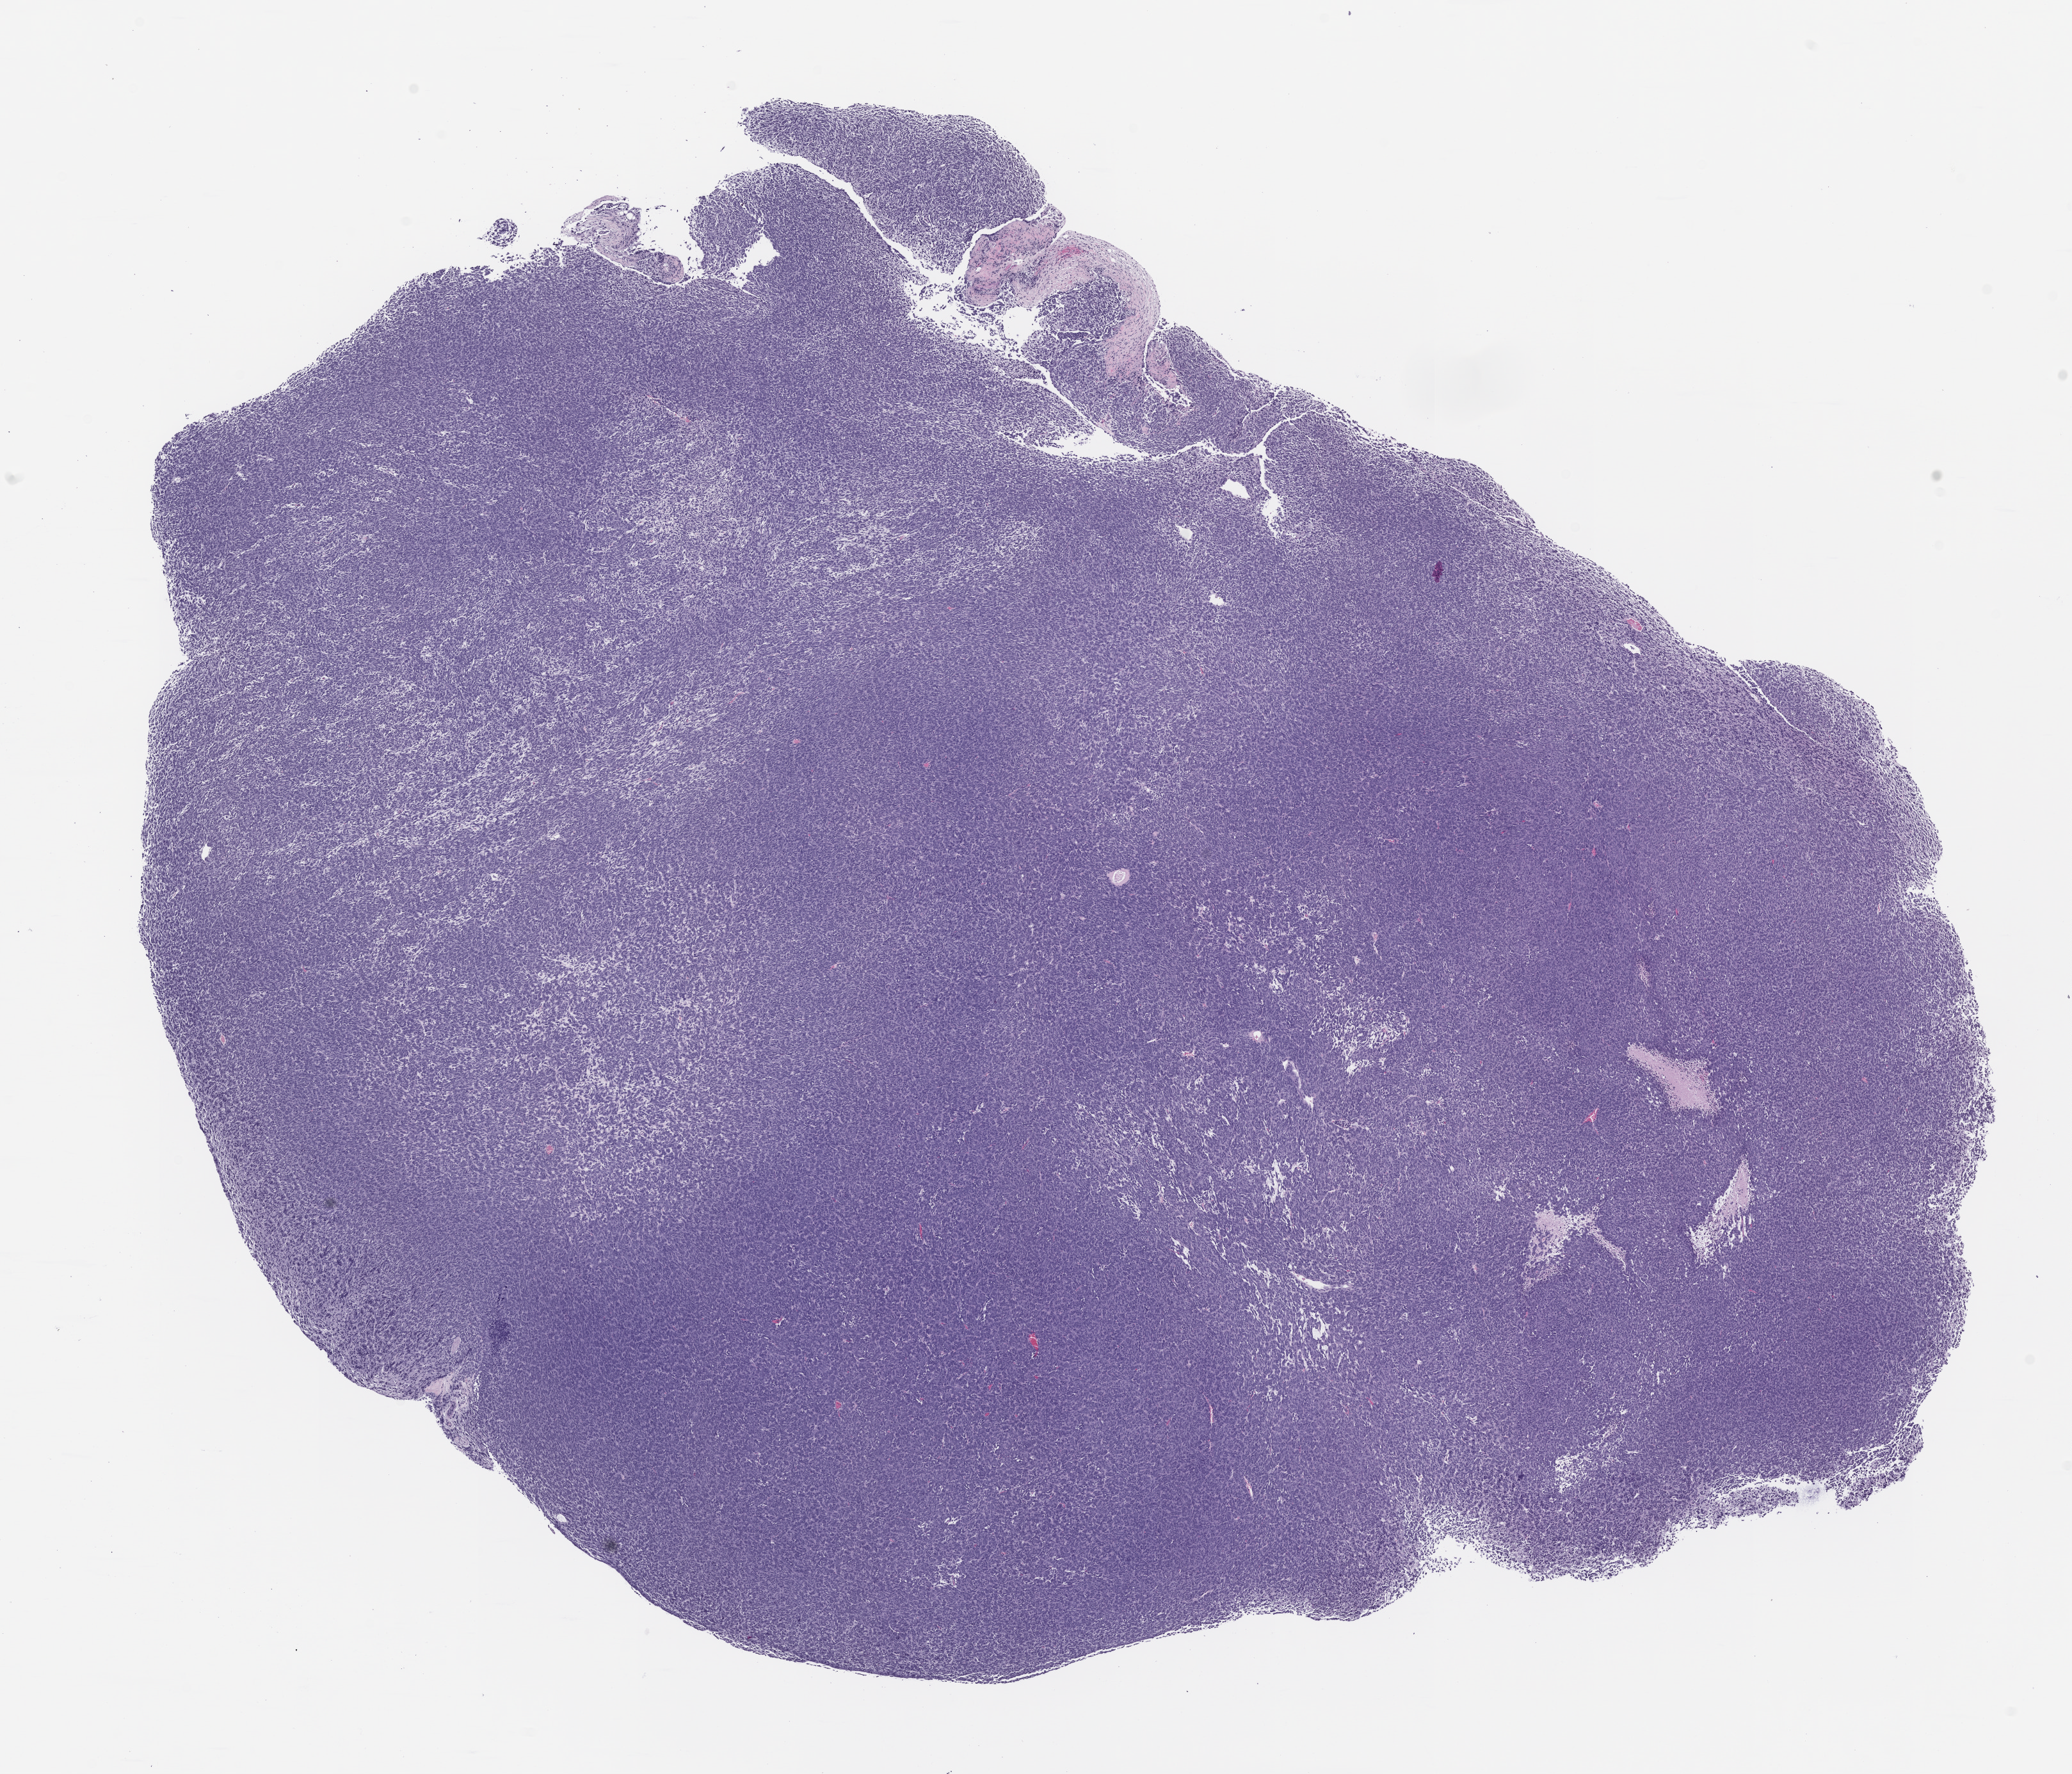
H&E whole-slide image of a patient-derived xenograft (PDX) tumor grown in a mouse, passage 1, a low-resolution overview of the entire scanned area, about 13.0 x 11.1 mm; formalin-fixed paraffin-embedded section; originating tumor site category: musculoskeletal.
Originating patient diagnosis: Synovial Sarcoma.